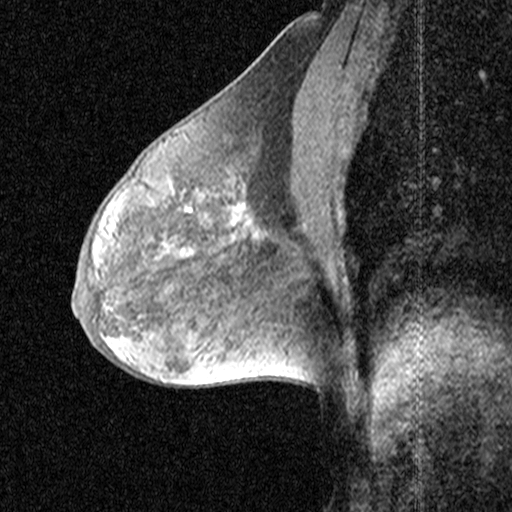
Breast MRI (dynamic contrast-enhanced), one sagittal slice; dynamic contrast-enhanced study with each time point stored as its own series, time point 2 of 3 at this slice position (early post-contrast, ordered by acquisition time); 1.5 T; TE 4.5 ms, TR 11 ms; 3 mm slice thickness; 512 × 512 image matrix. Patient: female, 53 years. From the clinical record (not read from this slice): setting: breast cancer imaged before/during neoadjuvant chemotherapy; receptor status: HR-positive, HER2-negative.
Annotated regions visible in this slice (semi-automatic segmentation, software-assisted and operator-edited):
- analysis volume of interest (the breast-tissue region the enhancement analysis was run in; not a lesion): bounding box <198,152,299,267> (left, top, right, bottom; pixels)
- tumour enhancement mask (voxels above the 90 % enhancement threshold inside the analysis volume of interest): <231,207,240,224>